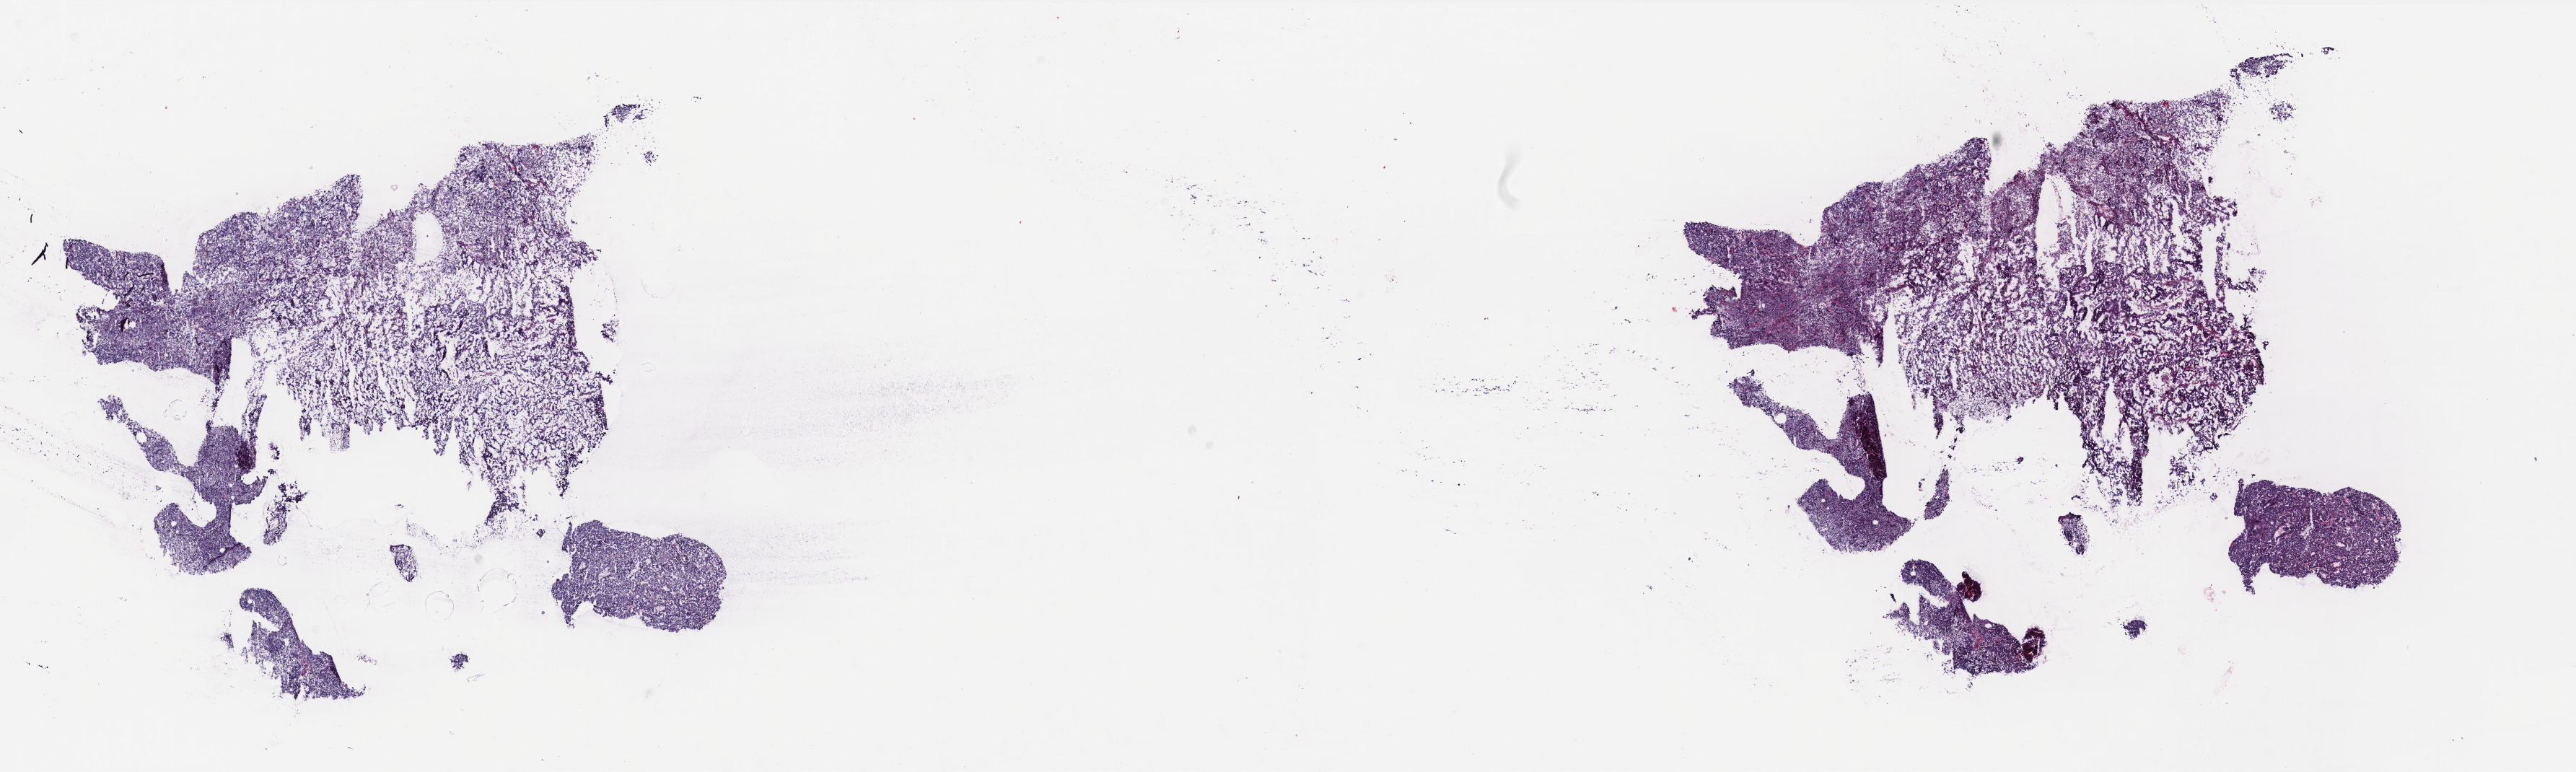
Digitized H&E-stained tissue section (whole slide), whole scanned area (about 28.6 x 8.6 mm, acquisition: 40x scan) shown as a low-resolution overview; frozen section; primary tumour sample from the uterus. Female patient; age at initial diagnosis 62 years.
Pathologic diagnosis: Endometrioid adenocarcinoma, NOS (endometrium).